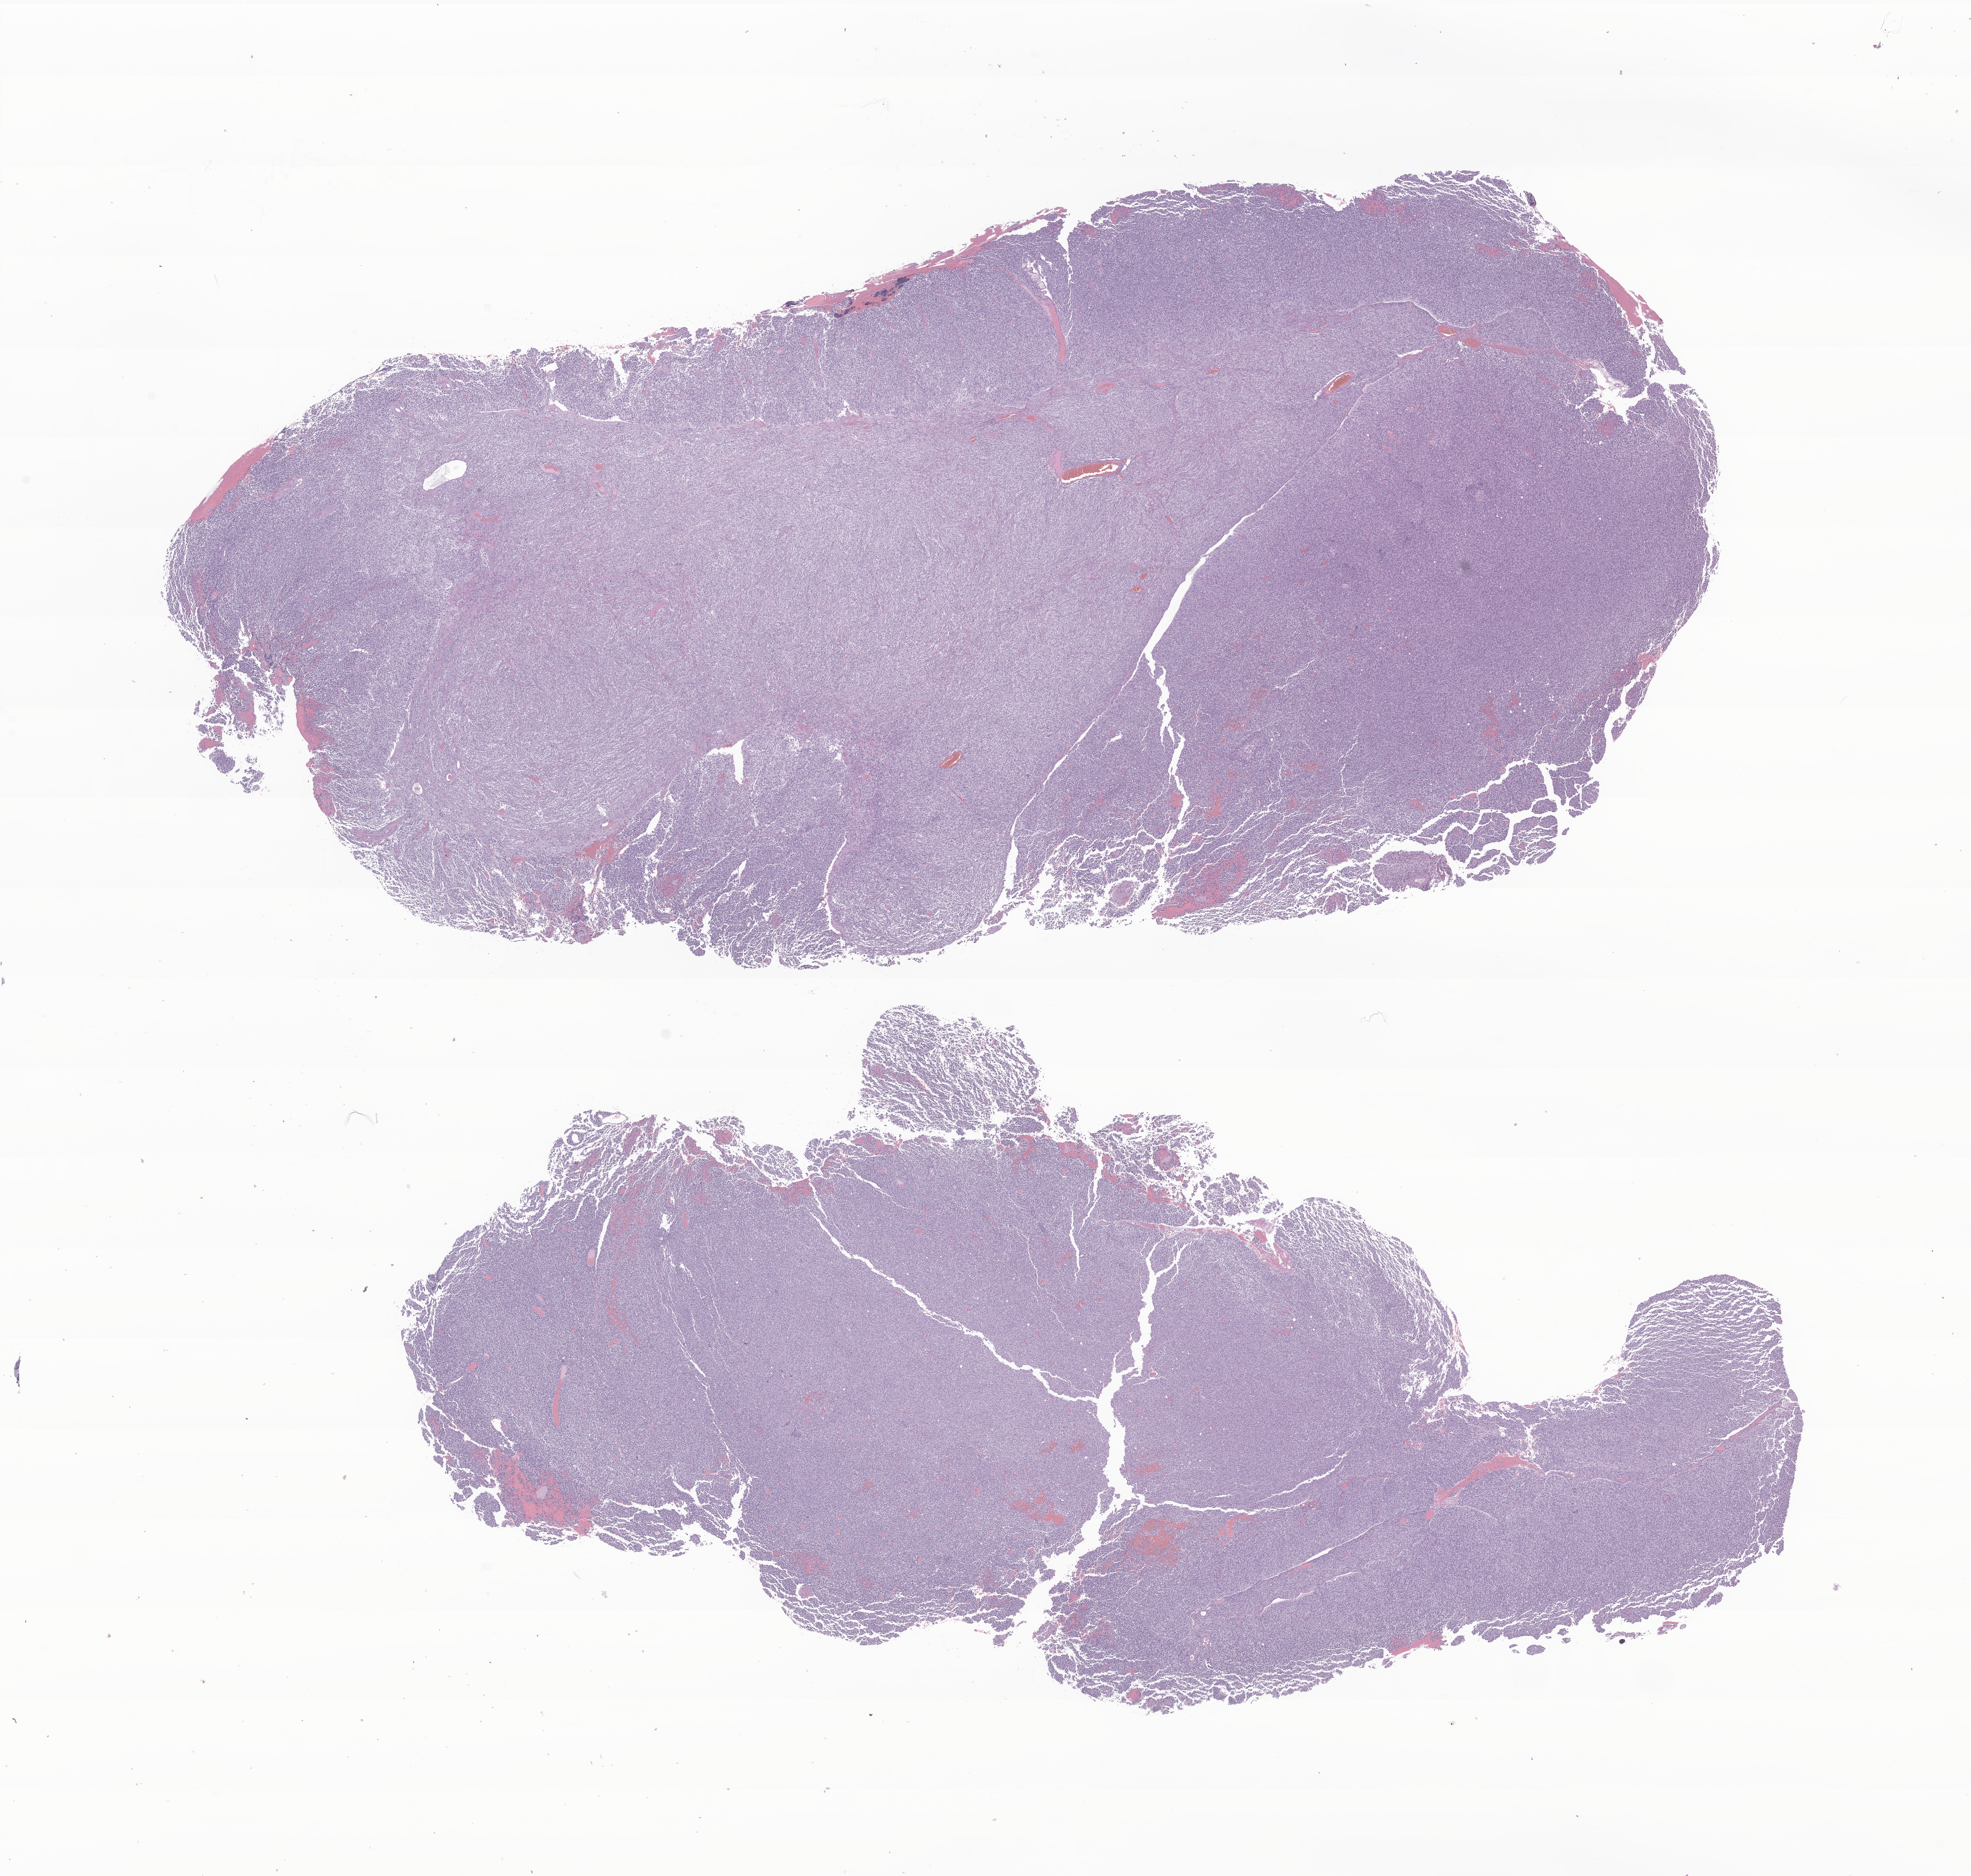
Digitized H&E-stained section of tumor tissue from the brain, a low-resolution overview of the entire scanned area, about 23.3 x 22.2 mm; formalin-fixed, paraffin-embedded (FFPE) tissue. Female patient, age 40 months (3 years 4 months).
• recorded diagnosis: Medulloblastoma, NOS